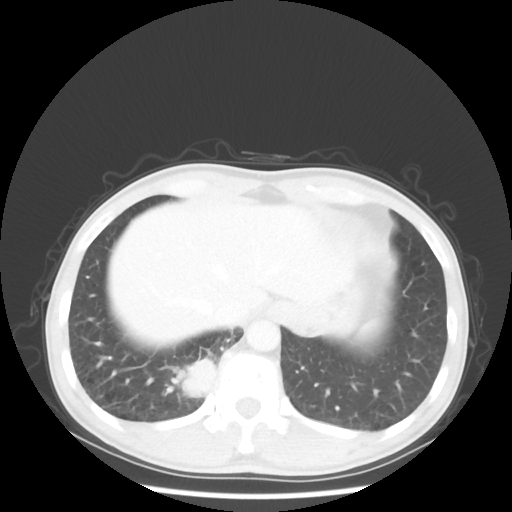
Chest CT, one axial slice. Slice 8 of 58 in the series (ordered by position). Reconstruction kernel STANDARD. 100 kVp. Lung window (W 1500 / L -600 HU). 5 mm slice thickness. 512 × 512 image matrix. Patient: male, 56 years. From the clinical record (not read from this slice): clinical TNM (as recorded): T2 N1 M1.
Structures marked on this image (rectangle marked by the reading radiologist):
- lung tumour (recorded histology: adenocarcinoma): bounding box (x1, y1, x2, y2) in pixels: (181, 355, 217, 400)